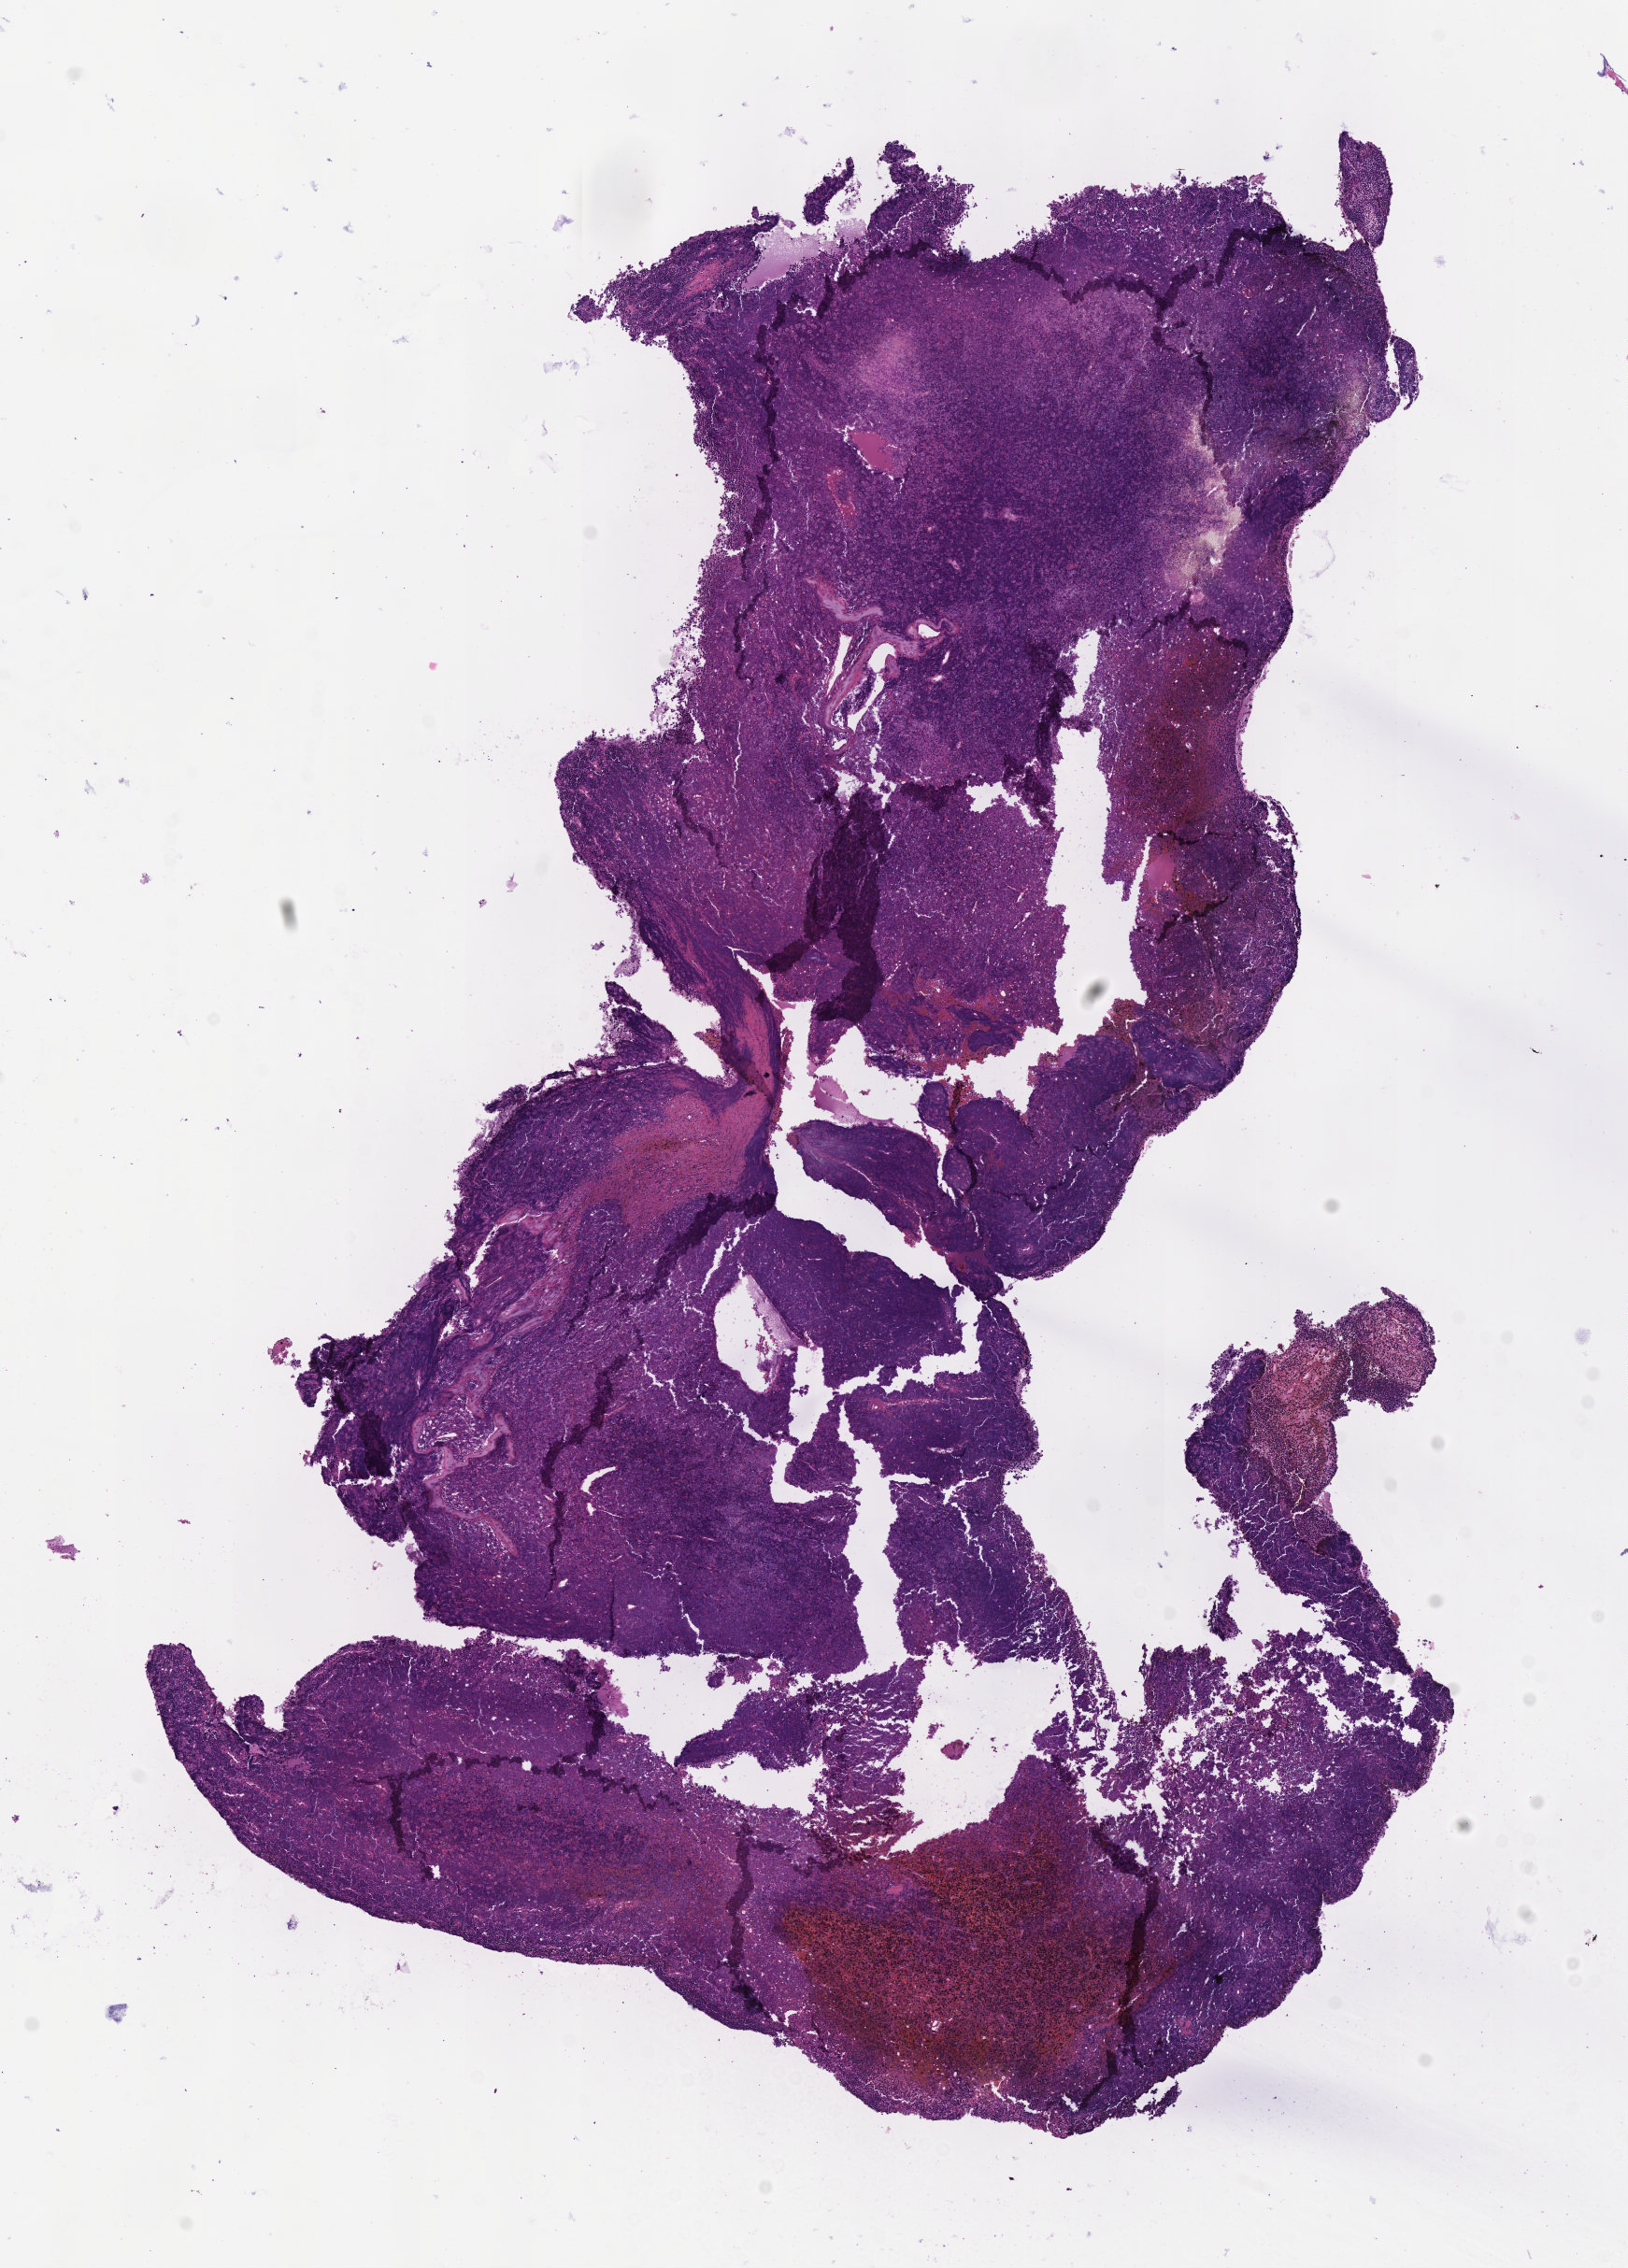
Digitized hematoxylin and eosin (H&E)-stained section, a low-resolution overview of the entire scanned area, about 7.0 x 9.8 mm. FFPE section. Primary tumor. Anatomic site: cranium. Patient female; aged 10. Slide review estimates, as recorded: tumor cells 90%, tumor nuclei 95%, stromal cells 5%, necrosis 5%, normal cells 0%. Inflammatory infiltration, as recorded: lymphocyte infiltration 10%, monocyte infiltration 30%, neutrophil infiltration 0%.
Ann Arbor stage (patient): Stage I. Diagnosis: Burkitt lymphoma, NOS. Section: top of the tissue portion.